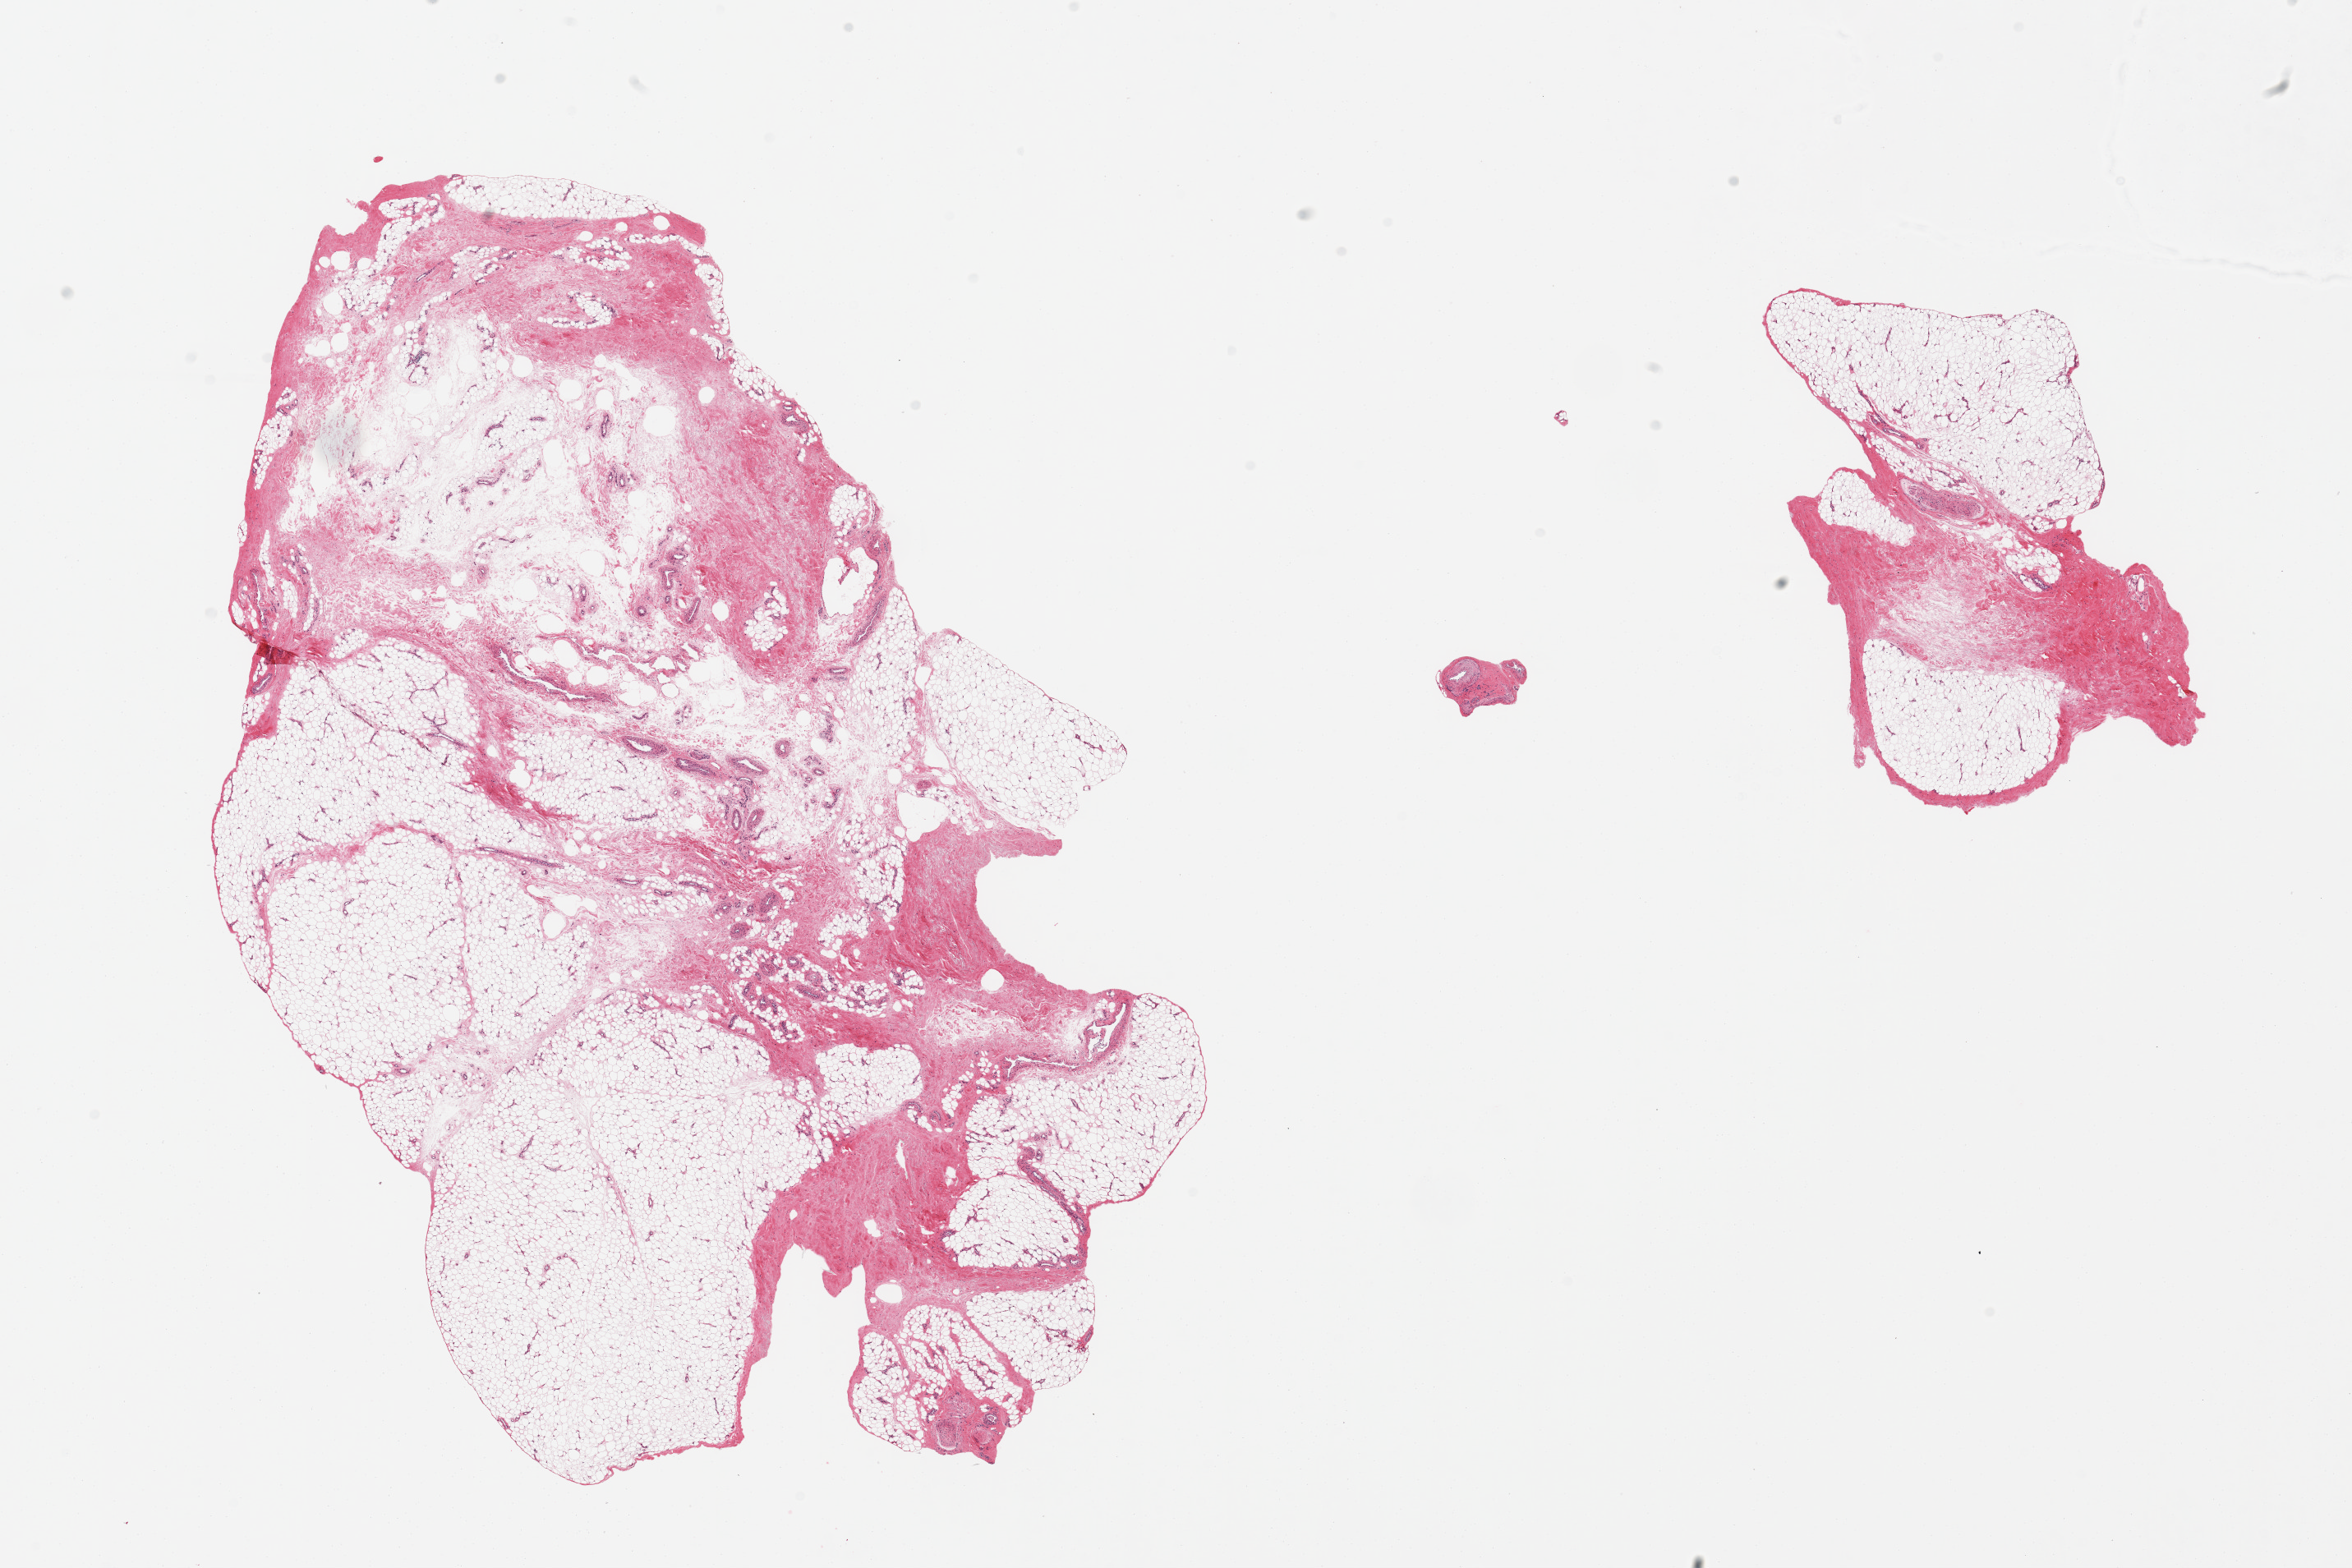
Hematoxylin and eosin (H&E) whole-slide image, brightfield — low-resolution overview of the scanned area, about 22.6 x 15.1 mm (slide scanned at 20x), PAXgene-fixed paraffin-embedded (PFPE) section, sampled site (target tissue): adipose tissue, donor tissue sample. Male donor.
Review note (as recorded): 2 pieces, 30-40% fascia.